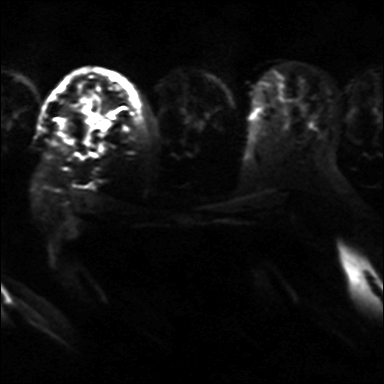
Breast MRI, one axial slice. Diffusion-weighted series; image 2 of 4 stored at this slice position (different b-values; order by instance number). 3 T. 4 mm slice thickness. 384 × 384 image matrix. Female patient.
Outlined on this slice (manually delineated by an expert):
- tumour on diffusion-weighted imaging: bounding box (x1, y1, x2, y2) in pixels: (79, 105, 111, 151)